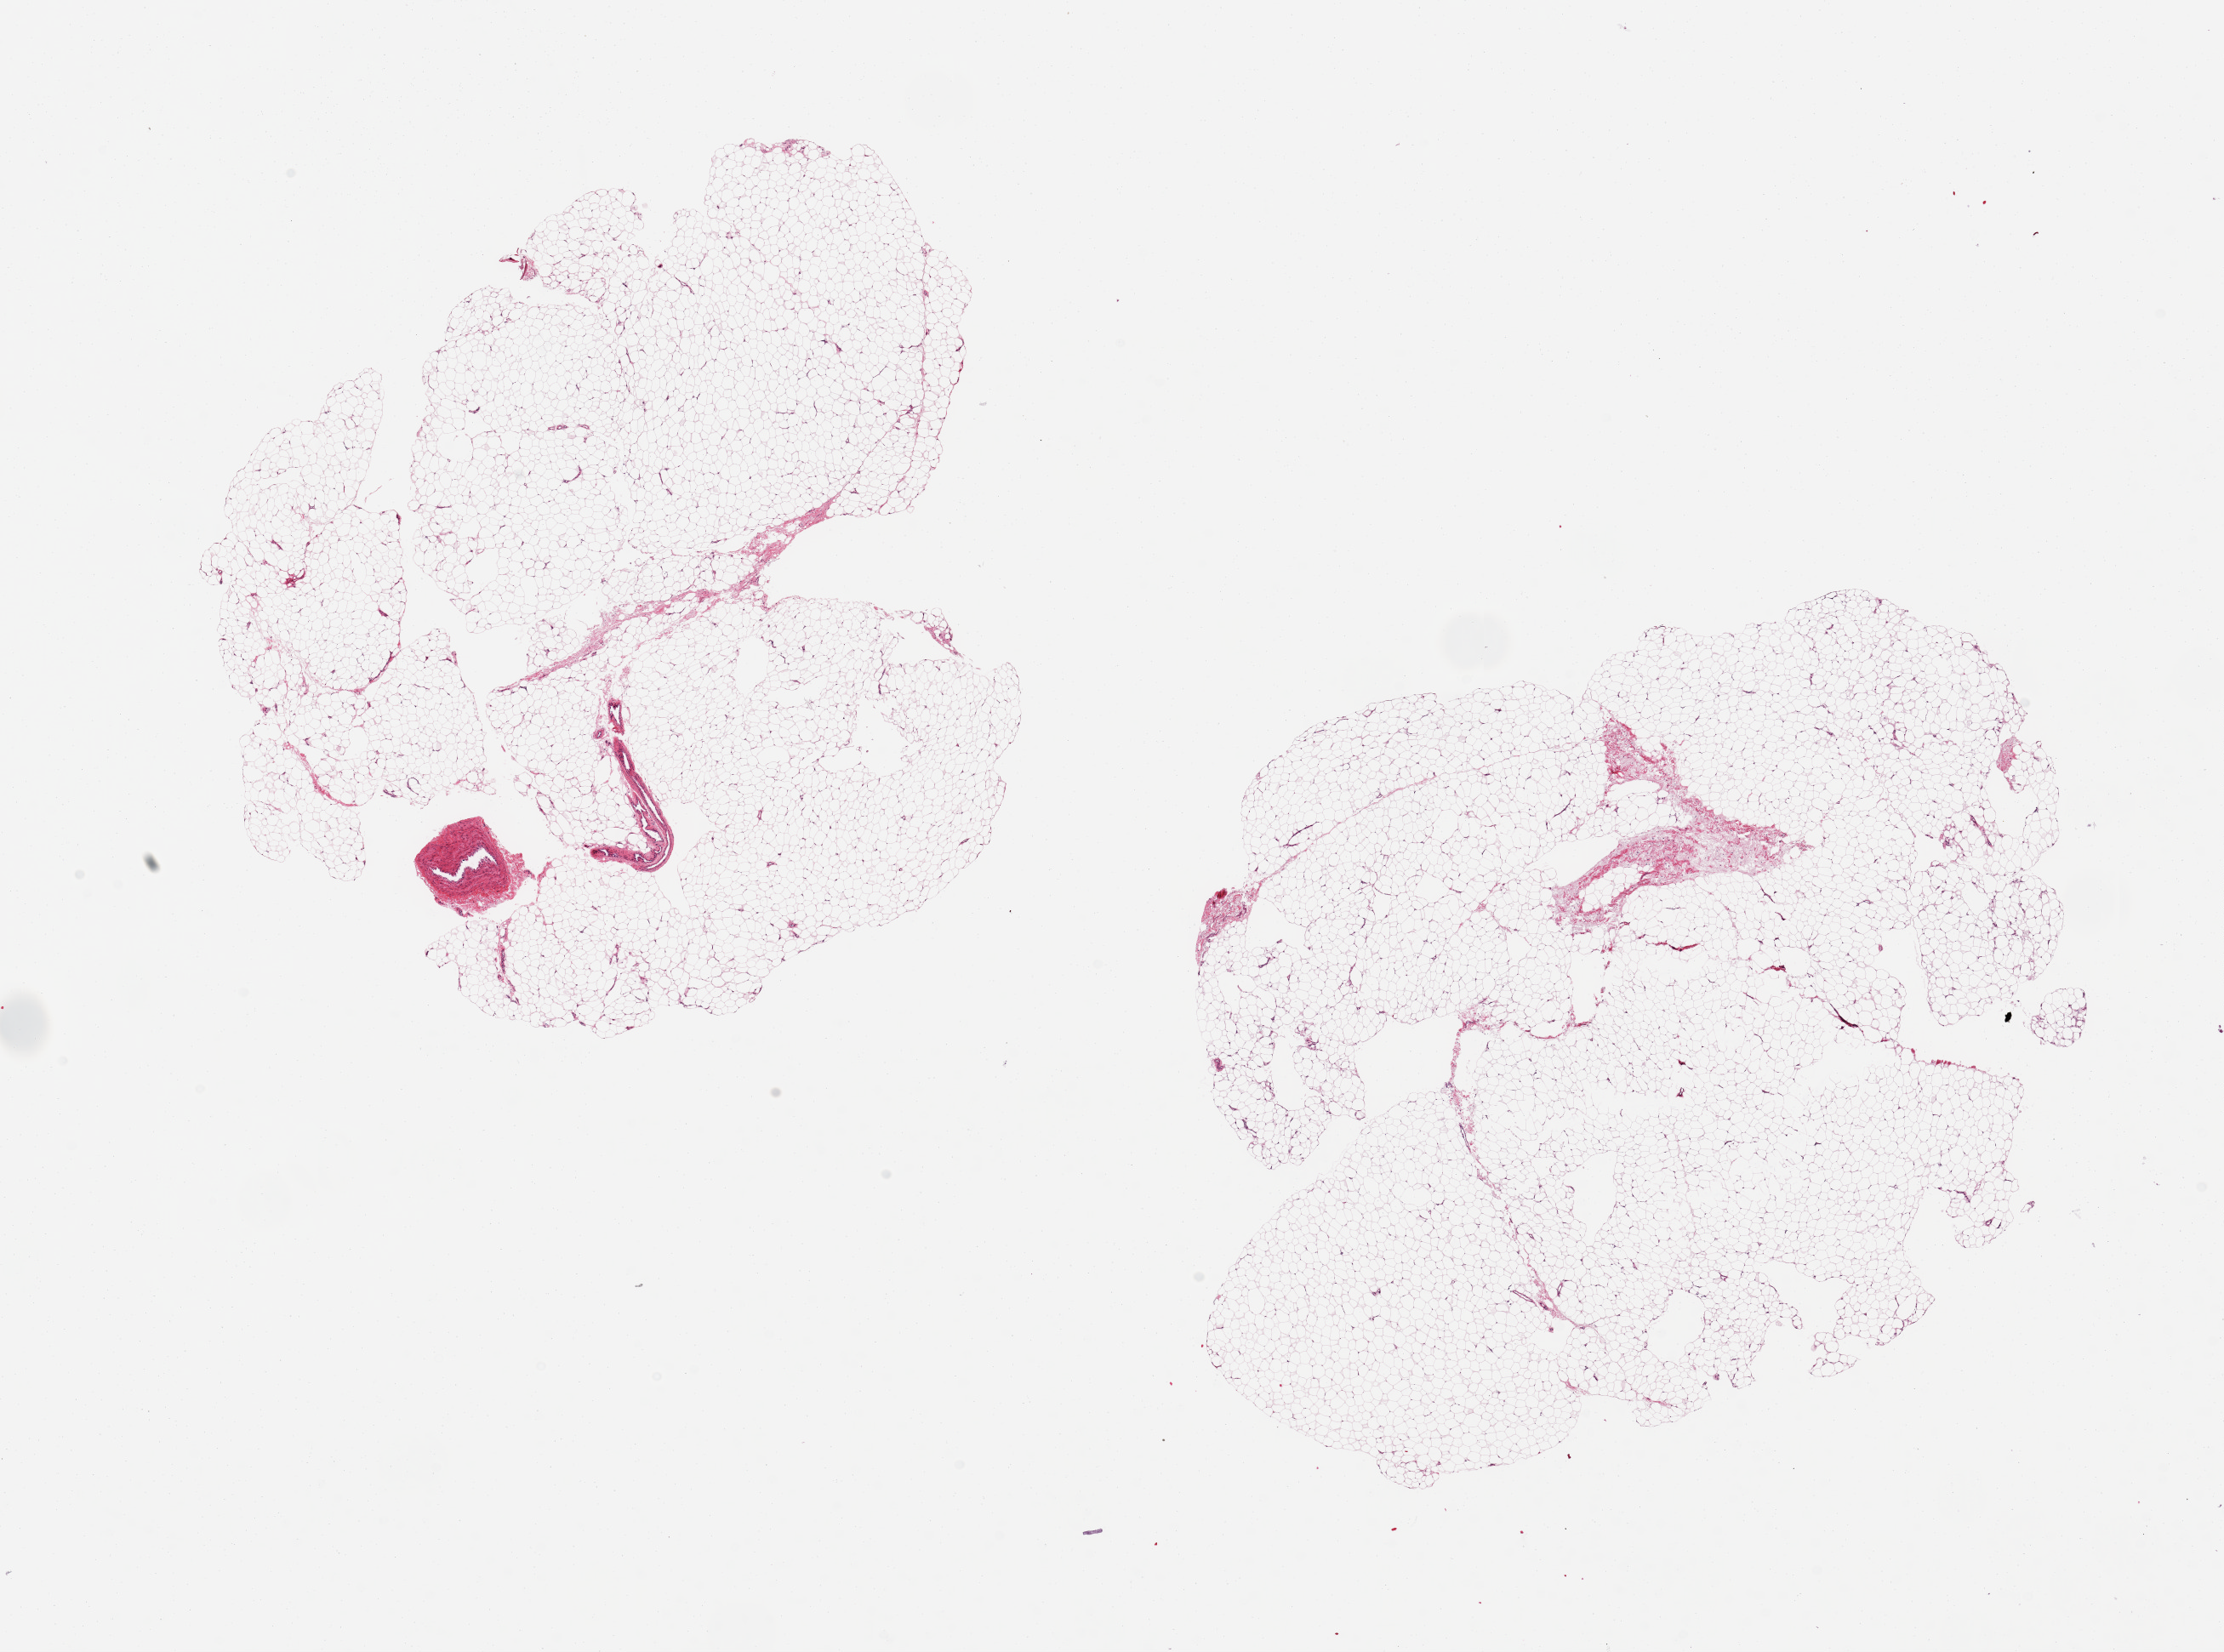
Digitized H&E-stained section, brightfield — low-resolution overview of the scanned area, about 20.7 x 15.4 mm (acquisition: 20x scan); PAXgene-fixed, paraffin-embedded tissue; sampled site (target tissue): adipose tissue; tissue donor sample. Donor: female.
- reviewer comment on this tissue sample: 2 pieces, 8x7 mm each; well fixed